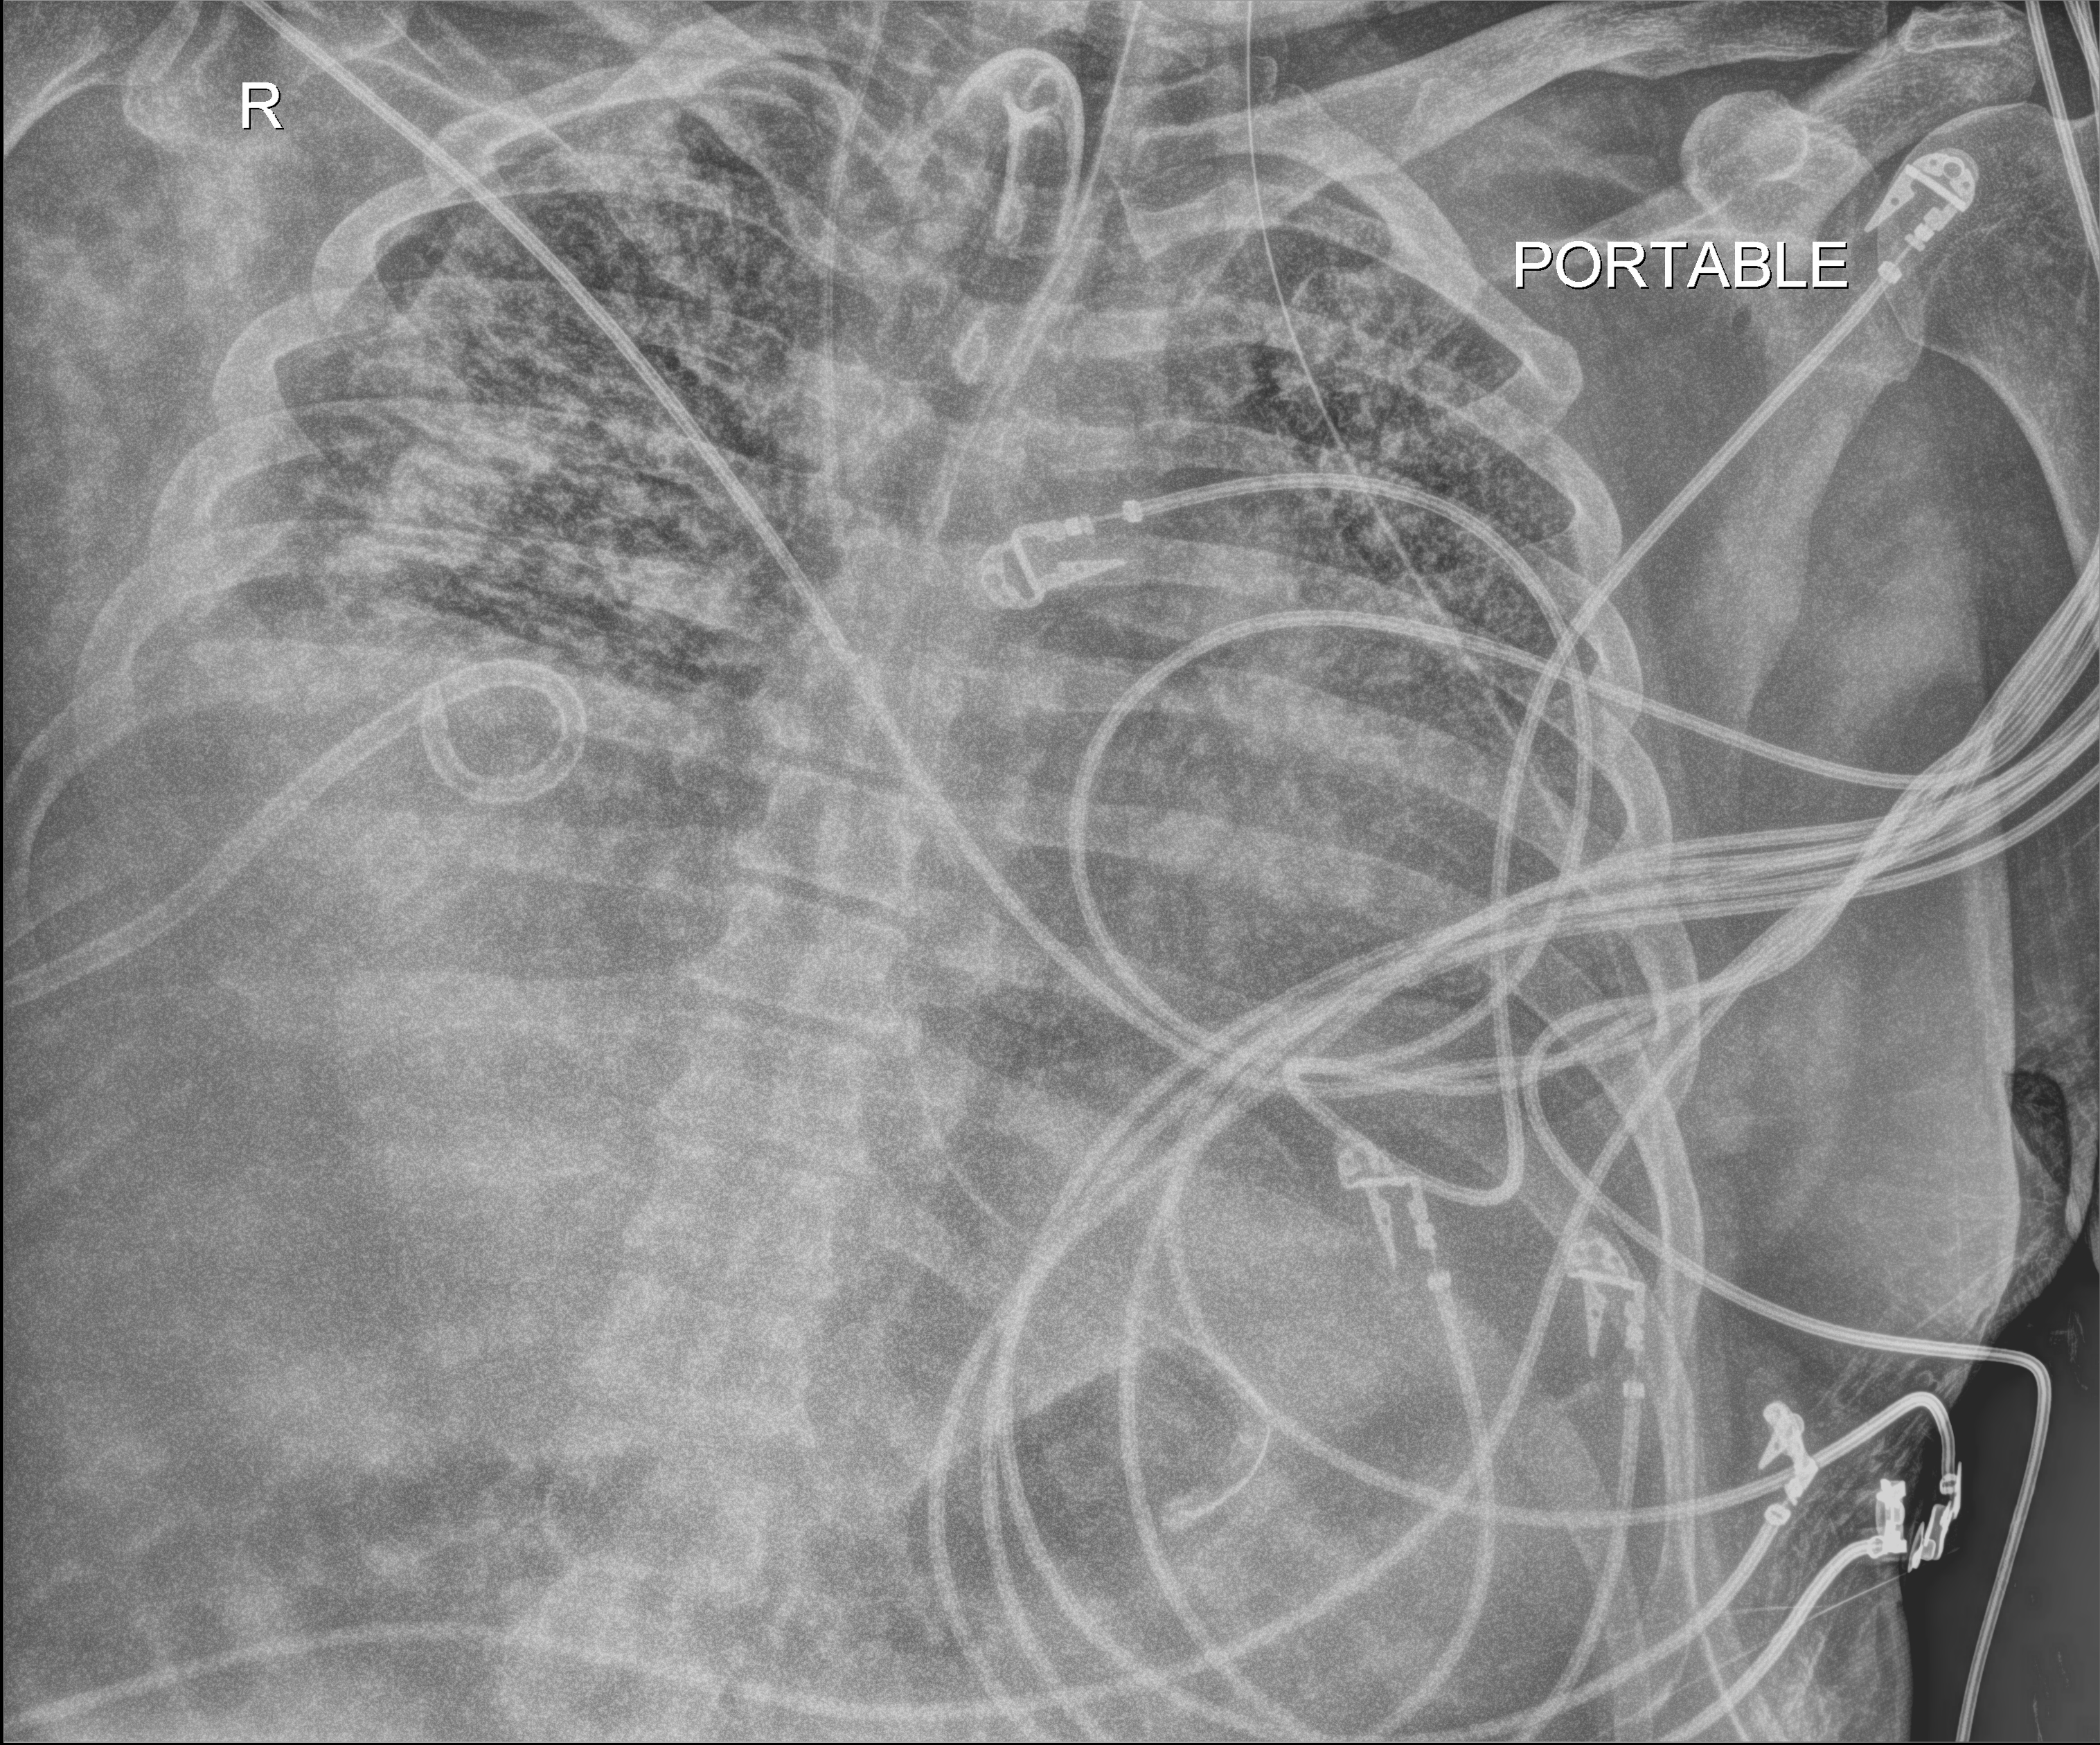
Portable chest radiograph; anteroposterior (AP) projection. Male patient hospitalised with COVID-19, age 18–59 years.
From the hospital-stay record, not from the radiograph (when in the stay this image was taken is not recorded): other chronic lung disease (admission record): no; admitted to intensive care during this hospital stay: yes.